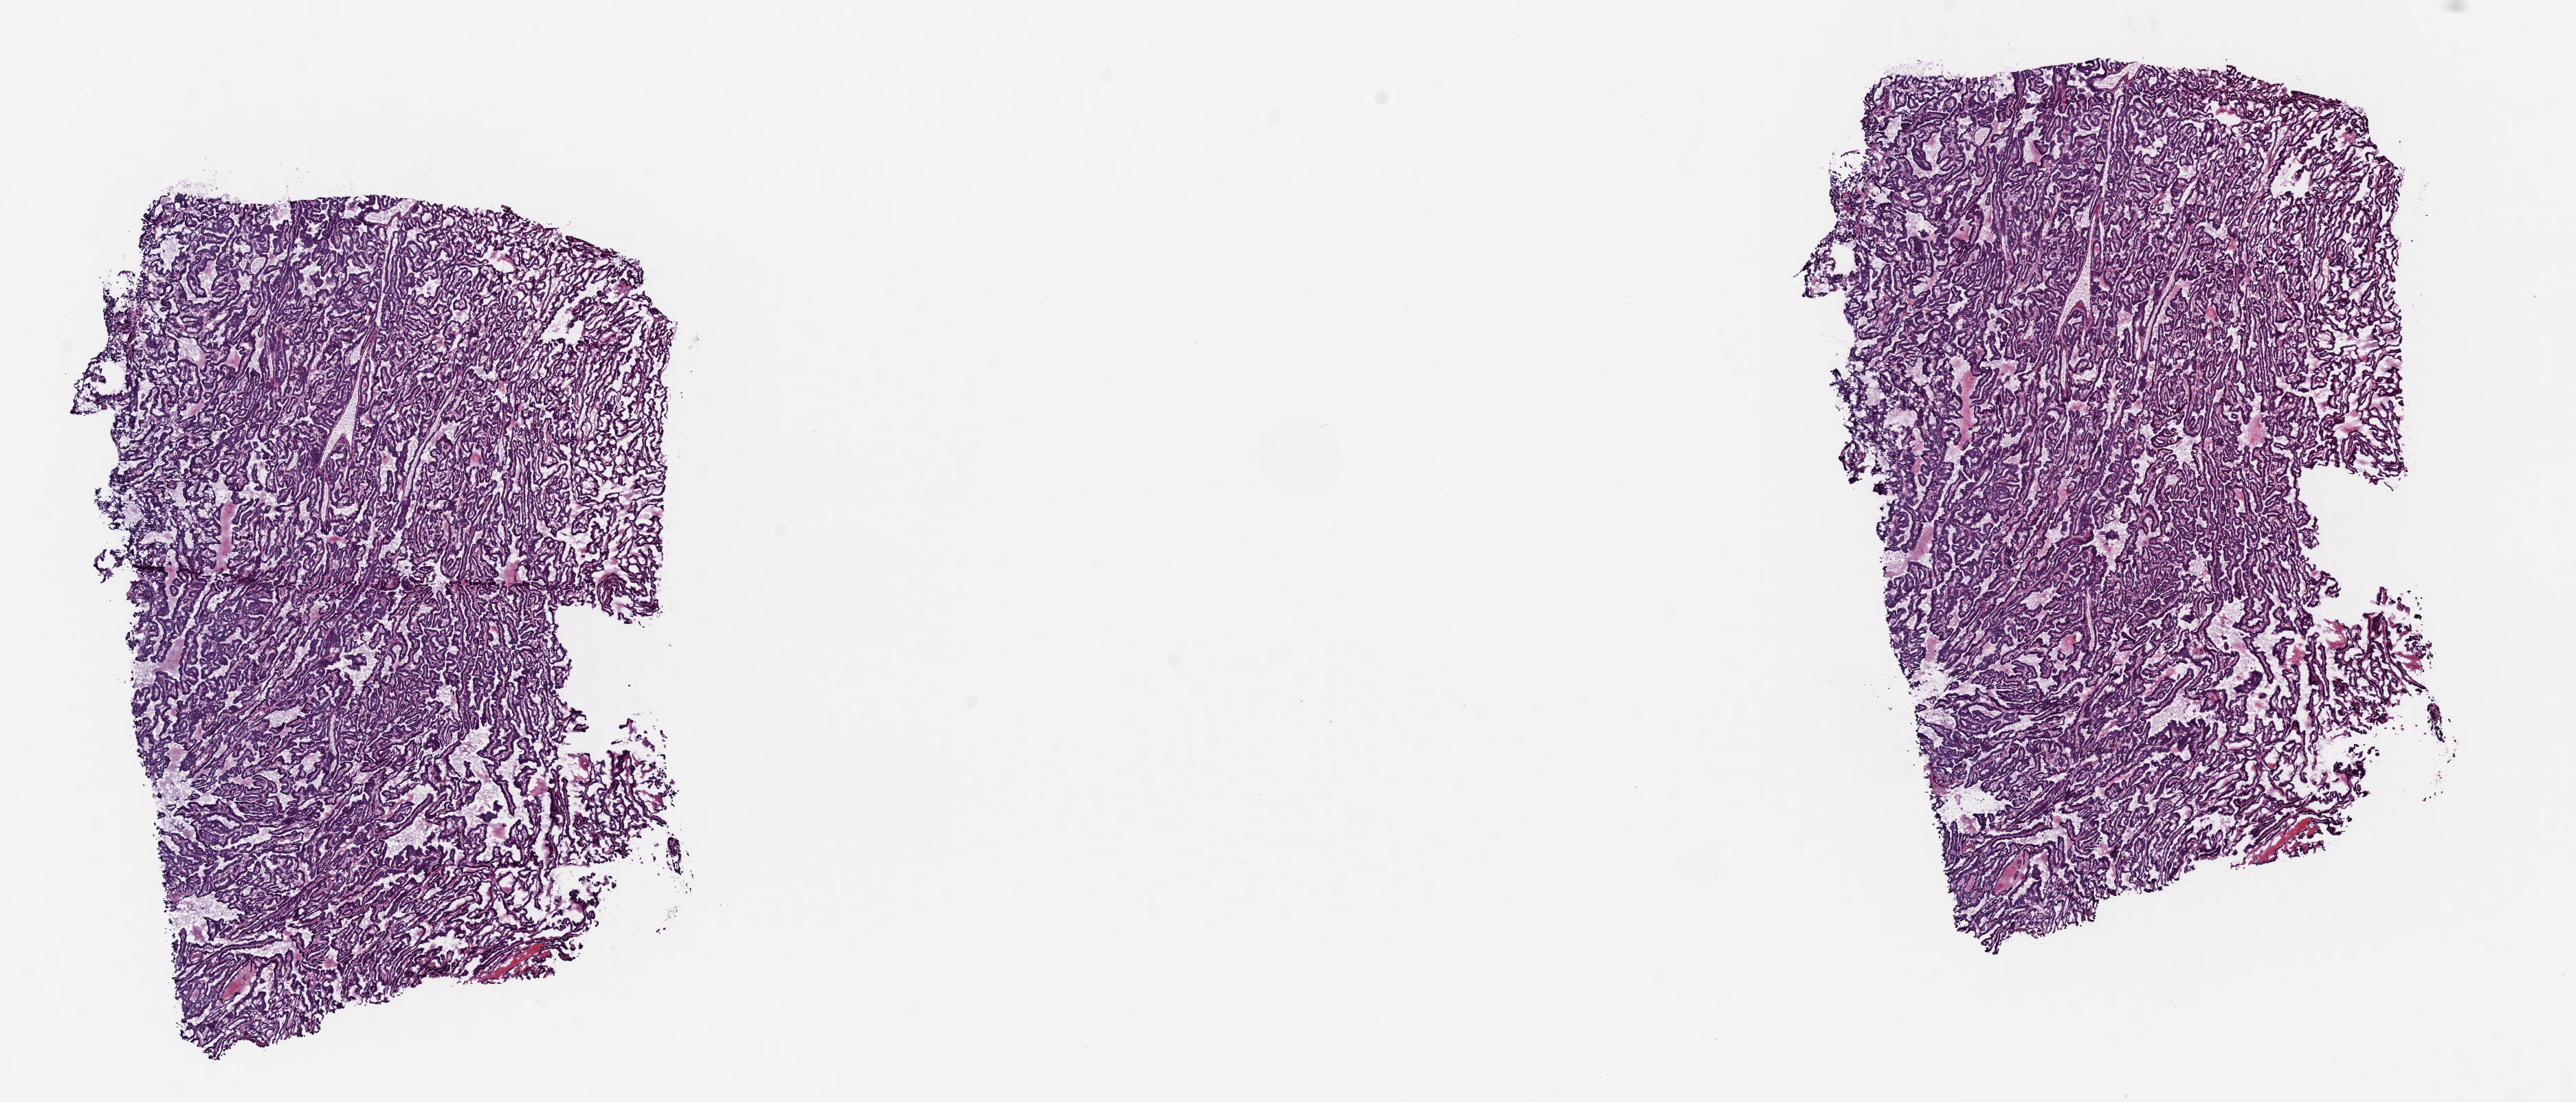
Digitized Hematoxylin and eosin (H&E) stained tissue section (whole slide) — whole scanned area (about 14.8 x 6.3 mm, from a 40x scan) shown as a low-resolution overview; frozen section; sample: primary tumour, thyroid. Female patient; age at initial diagnosis 35 years. Slide review estimates, as recorded: tumour cells 100%, tumour nuclei 94%, normal cells 0%, stromal cells 0%, necrosis 0%. Infiltration values recorded for this section: lymphocyte infiltration 0%, monocyte infiltration 0%, neutrophil infiltration 0%.
Histologic diagnosis: Papillary adenocarcinoma, NOS (thyroid gland). TNM: T2 N1a MX. Lymph nodes positive (case pathology): 2 of 5 examined. AJCC pathologic stage: I.